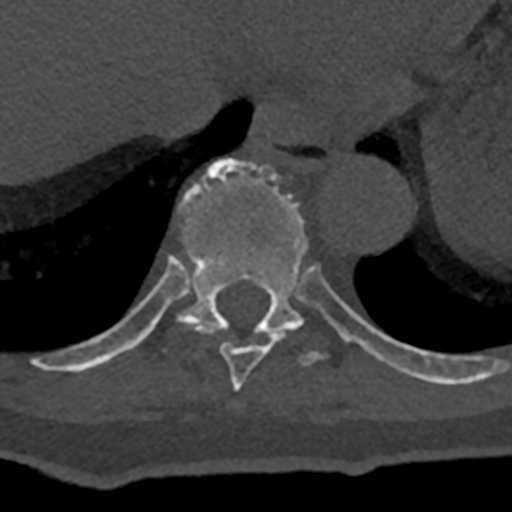
CT including the spine, one axial slice. Position 624 of 797 along the scan axis. Reconstruction kernel Br40s/3. Bone window (W 1800 / L 400 HU). 0.5 mm slice thickness. 512 × 512 image matrix, field of view 160 × 160 mm. Male patient, age 74 years. Case-level facts recorded for this patient, not image findings: primary cancer: renal; vertebrae with lytic lesions (as recorded): T10, L1, L2, L3, L4, L5.
Structures marked on this image (semi-automatic segmentation, software-assisted and operator-edited):
- T10 vertebra: bounding box <70,158,432,382> (left, top, right, bottom; pixels)
- T9 vertebra: <179,320,284,391>